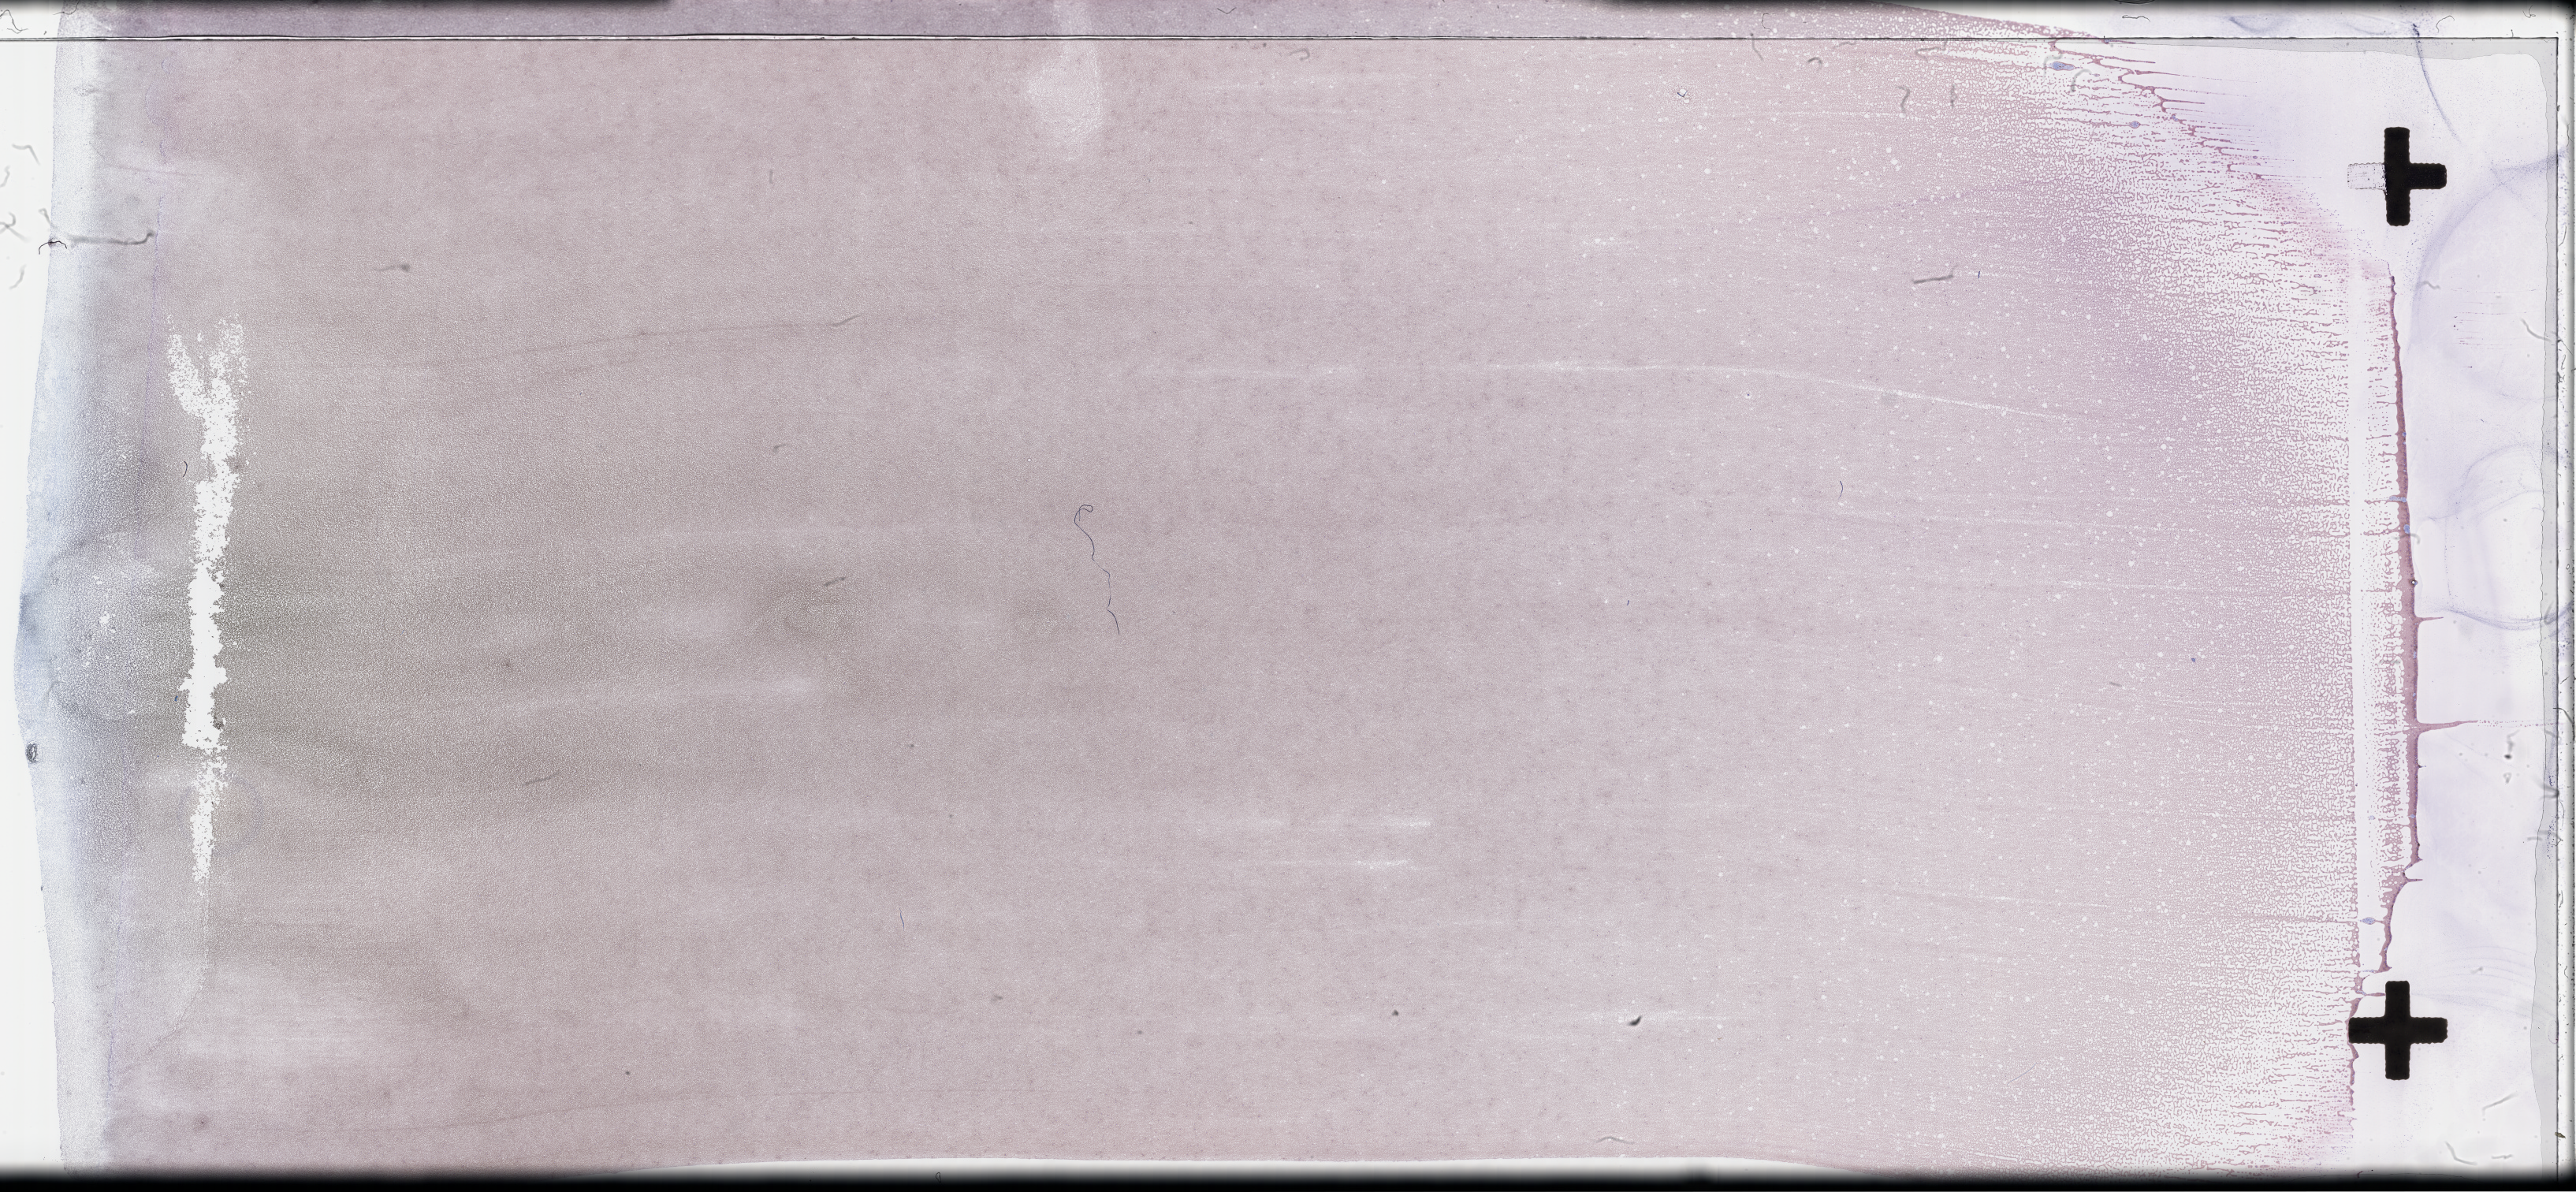
Wright-Giemsa-stained whole blood smear, whole-slide image — shown as a low-resolution overview of the whole scanned area (about 52.8 x 24.4 mm); smear from an EDTA sample; collected on treatment. Patient: male.
From a patient with: Plasma Cell Myeloma.